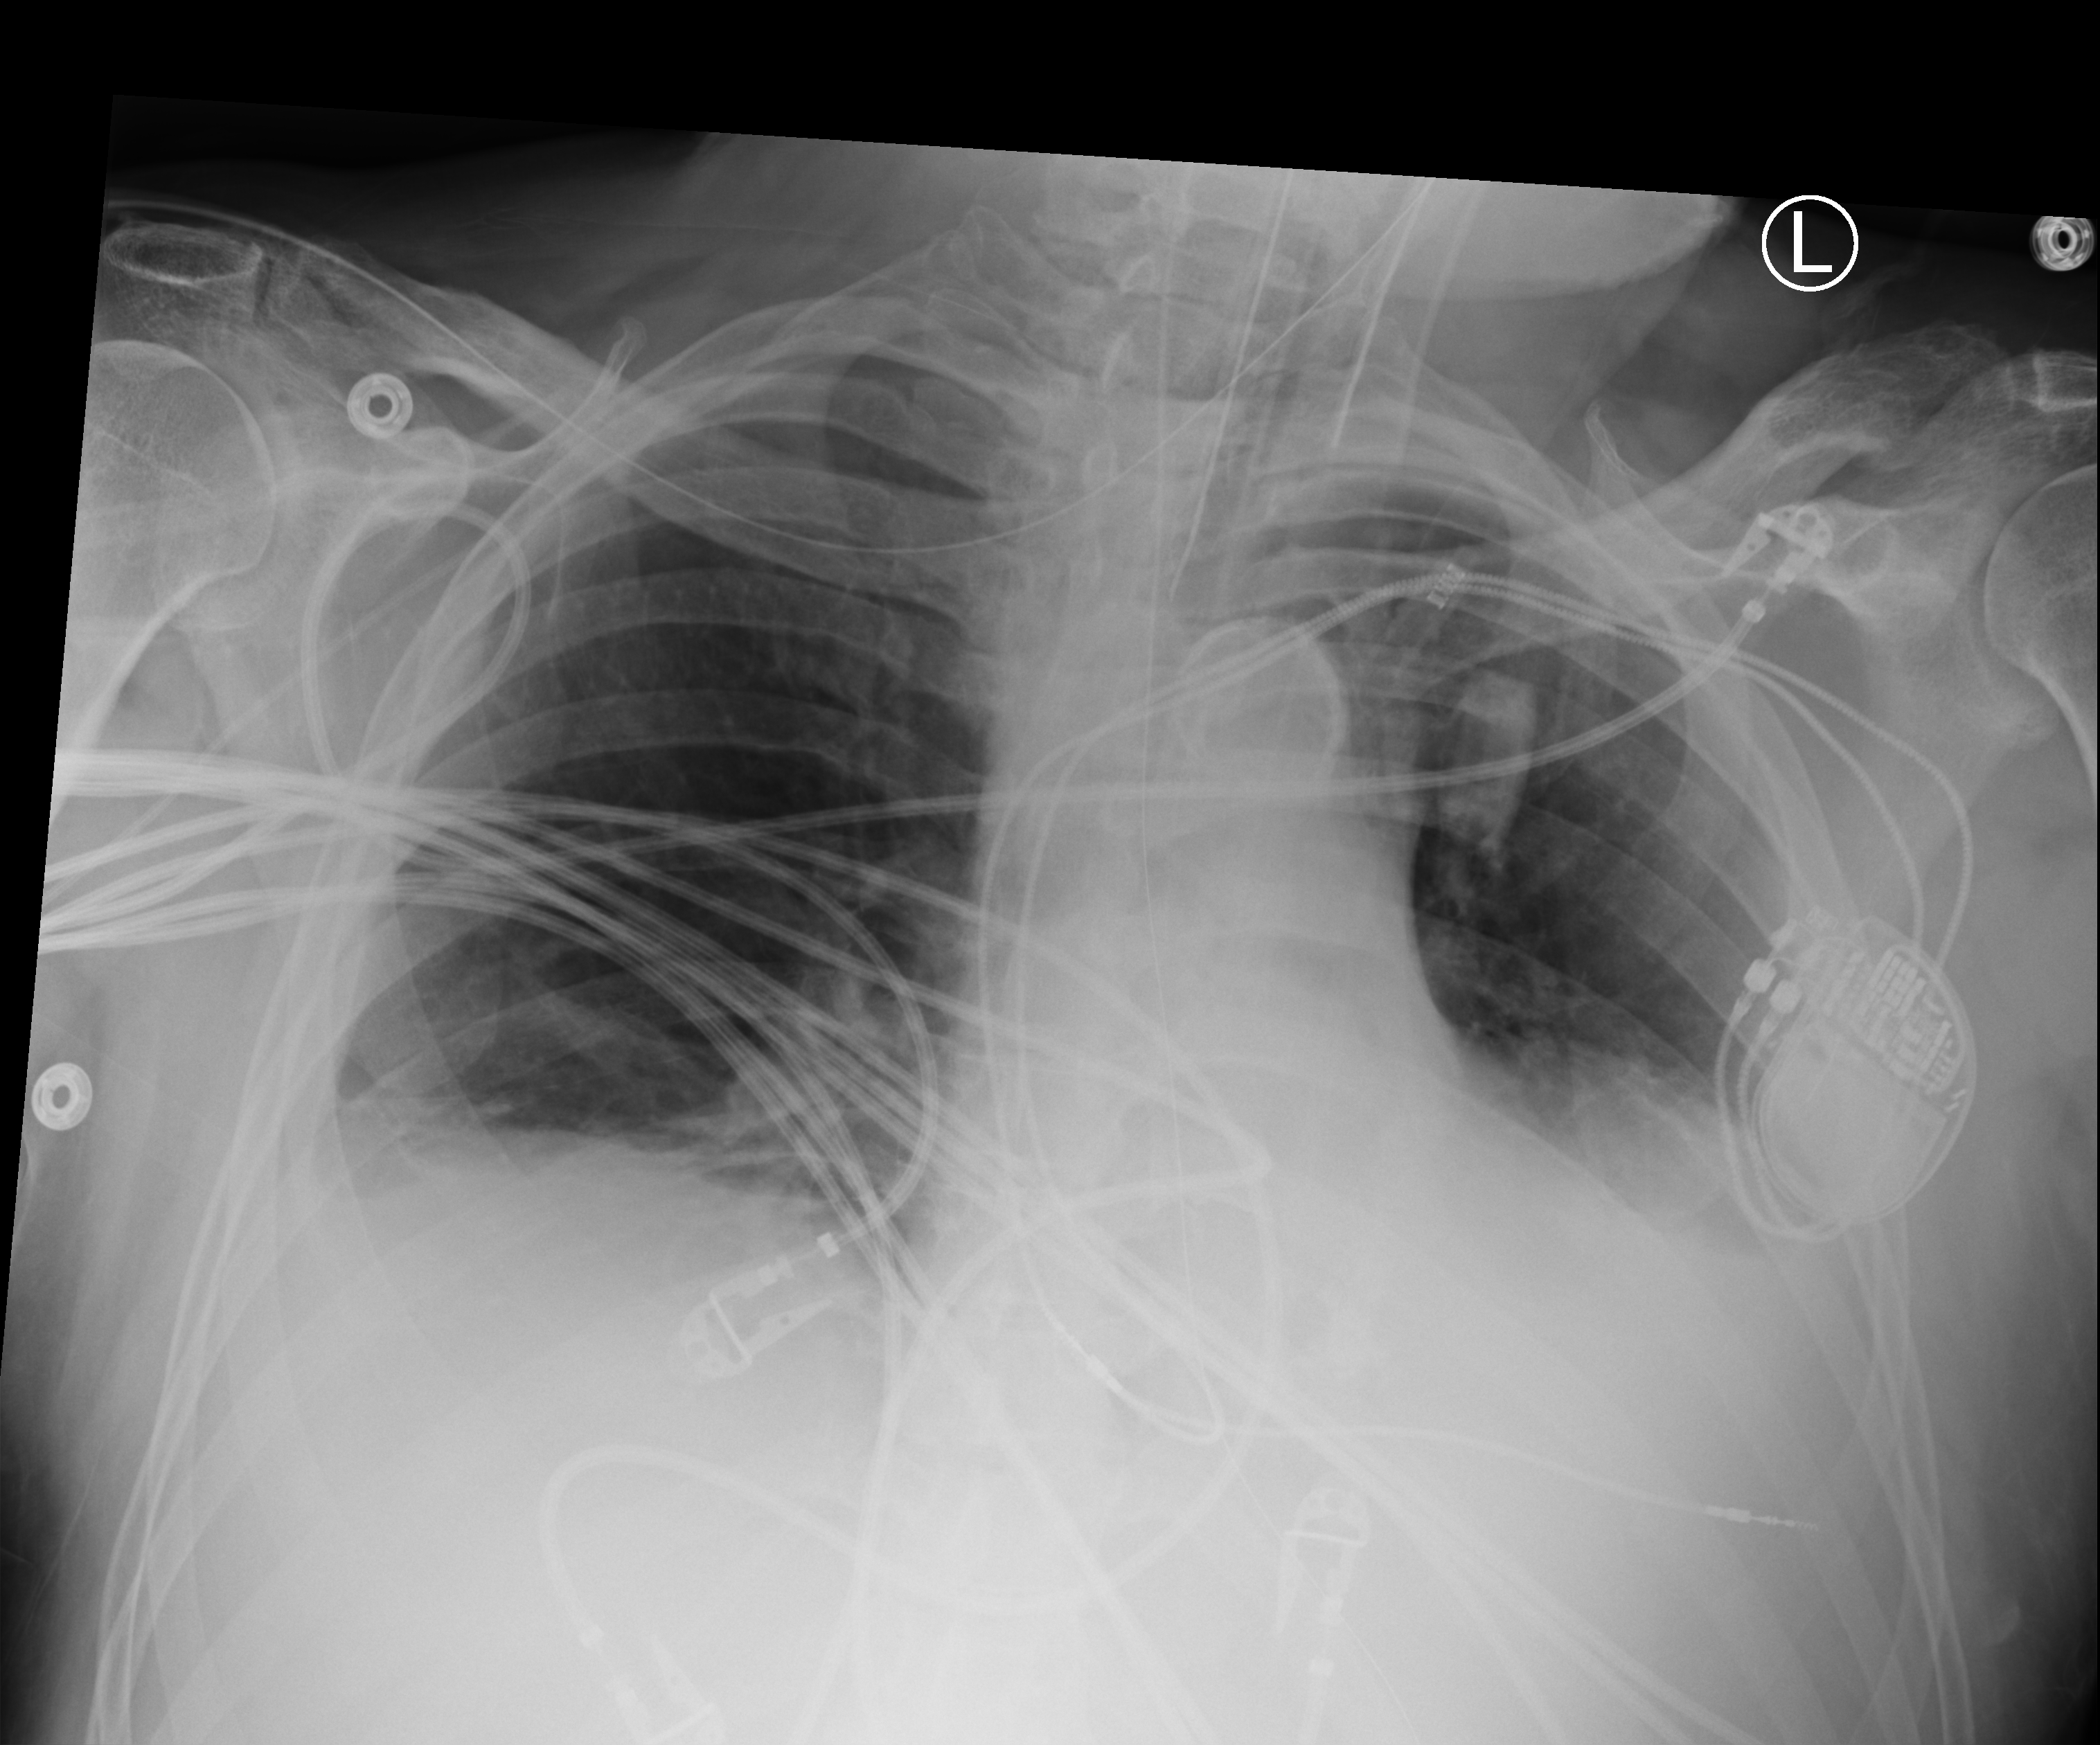
Bedside chest radiograph (computed radiography); anteroposterior (AP) projection. Male patient hospitalised with COVID-19, age 60–74 years.
Hospital-stay facts (about this admission, not read from this image; timing relative to this image not recorded):
- admitted to intensive care during this hospital stay: yes